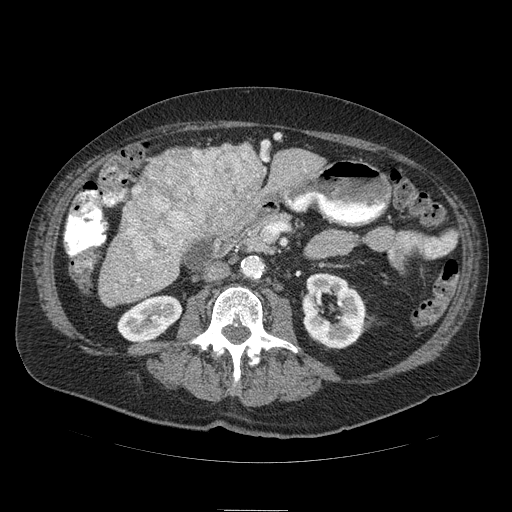
Contrast-enhanced abdominal CT (liver protocol), one axial slice; slice 26 of 103 in the series (ordered by position); reconstruction kernel STANDARD; soft-tissue window (W 400 / L 40 HU); 512 × 512 image matrix, field of view 440 × 440 mm. Case-level facts recorded for this patient, not image findings: diagnosis: hepatocellular carcinoma (patient treated with transarterial chemoembolisation; whether this scan precedes or follows treatment is not stated here); TNM stage (as recorded): Stage-IIIA; Child-Pugh class: B; tumour differentiation: well differentiated.
Structures marked on this image (semi-automatically segmented with operator editing):
- liver parenchyma outside the tumour (the mass and vessels are separate outlines, so this box may not span the whole liver): bounding box (x1, y1, x2, y2) in pixels: (100, 140, 324, 300)
- mass: (125, 143, 267, 270)
- liver vessels: (129, 141, 269, 281)